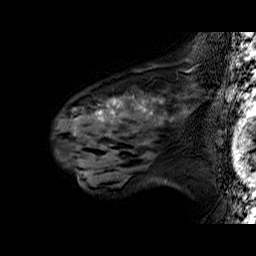
Breast MRI (dynamic contrast-enhanced), one sagittal slice. Slice 43 of 60 in the series (ordered by position). Dynamic contrast-enhanced series, time point 2 of 6 at this slice position (early post-contrast). 1.5 T. TE 6.4 ms, TR 32.9 ms. 4 mm slice thickness. 256 × 256 image matrix, field of view 200 × 200 mm. Female patient. From the clinical record (not read from this slice): setting: breast cancer imaged before/during neoadjuvant chemotherapy; receptor status: HER2-positive.
Annotated regions visible in this slice (semi-automatically segmented with operator editing):
- analysis volume of interest (the breast-tissue region the enhancement analysis was run in; not a lesion): bounding box [x1, y1, x2, y2] px = [54, 78, 196, 160]
- tumour enhancement mask (voxels above the 100 % enhancement threshold inside the analysis volume of interest): [95, 97, 156, 121]